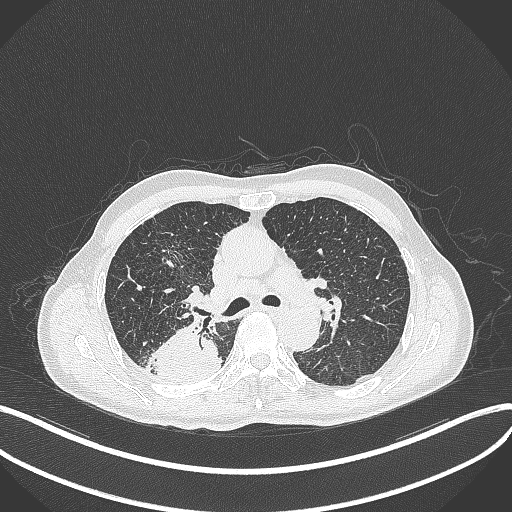
Chest CT, one axial slice. Position 293 of 428 along the scan axis. 120 kVp. Lung window (W 1500 / L -600 HU). 1 mm slice thickness. 512 × 512 image matrix. Male patient, age 79 years. Case-level facts recorded for this patient, not image findings: clinical TNM (as recorded): T3 N0 M0.
Outlined on this slice (bounding box drawn by a radiologist):
- lung tumour (recorded histology: adenocarcinoma): bounding box (x1, y1, x2, y2) in pixels: (151, 328, 224, 384)